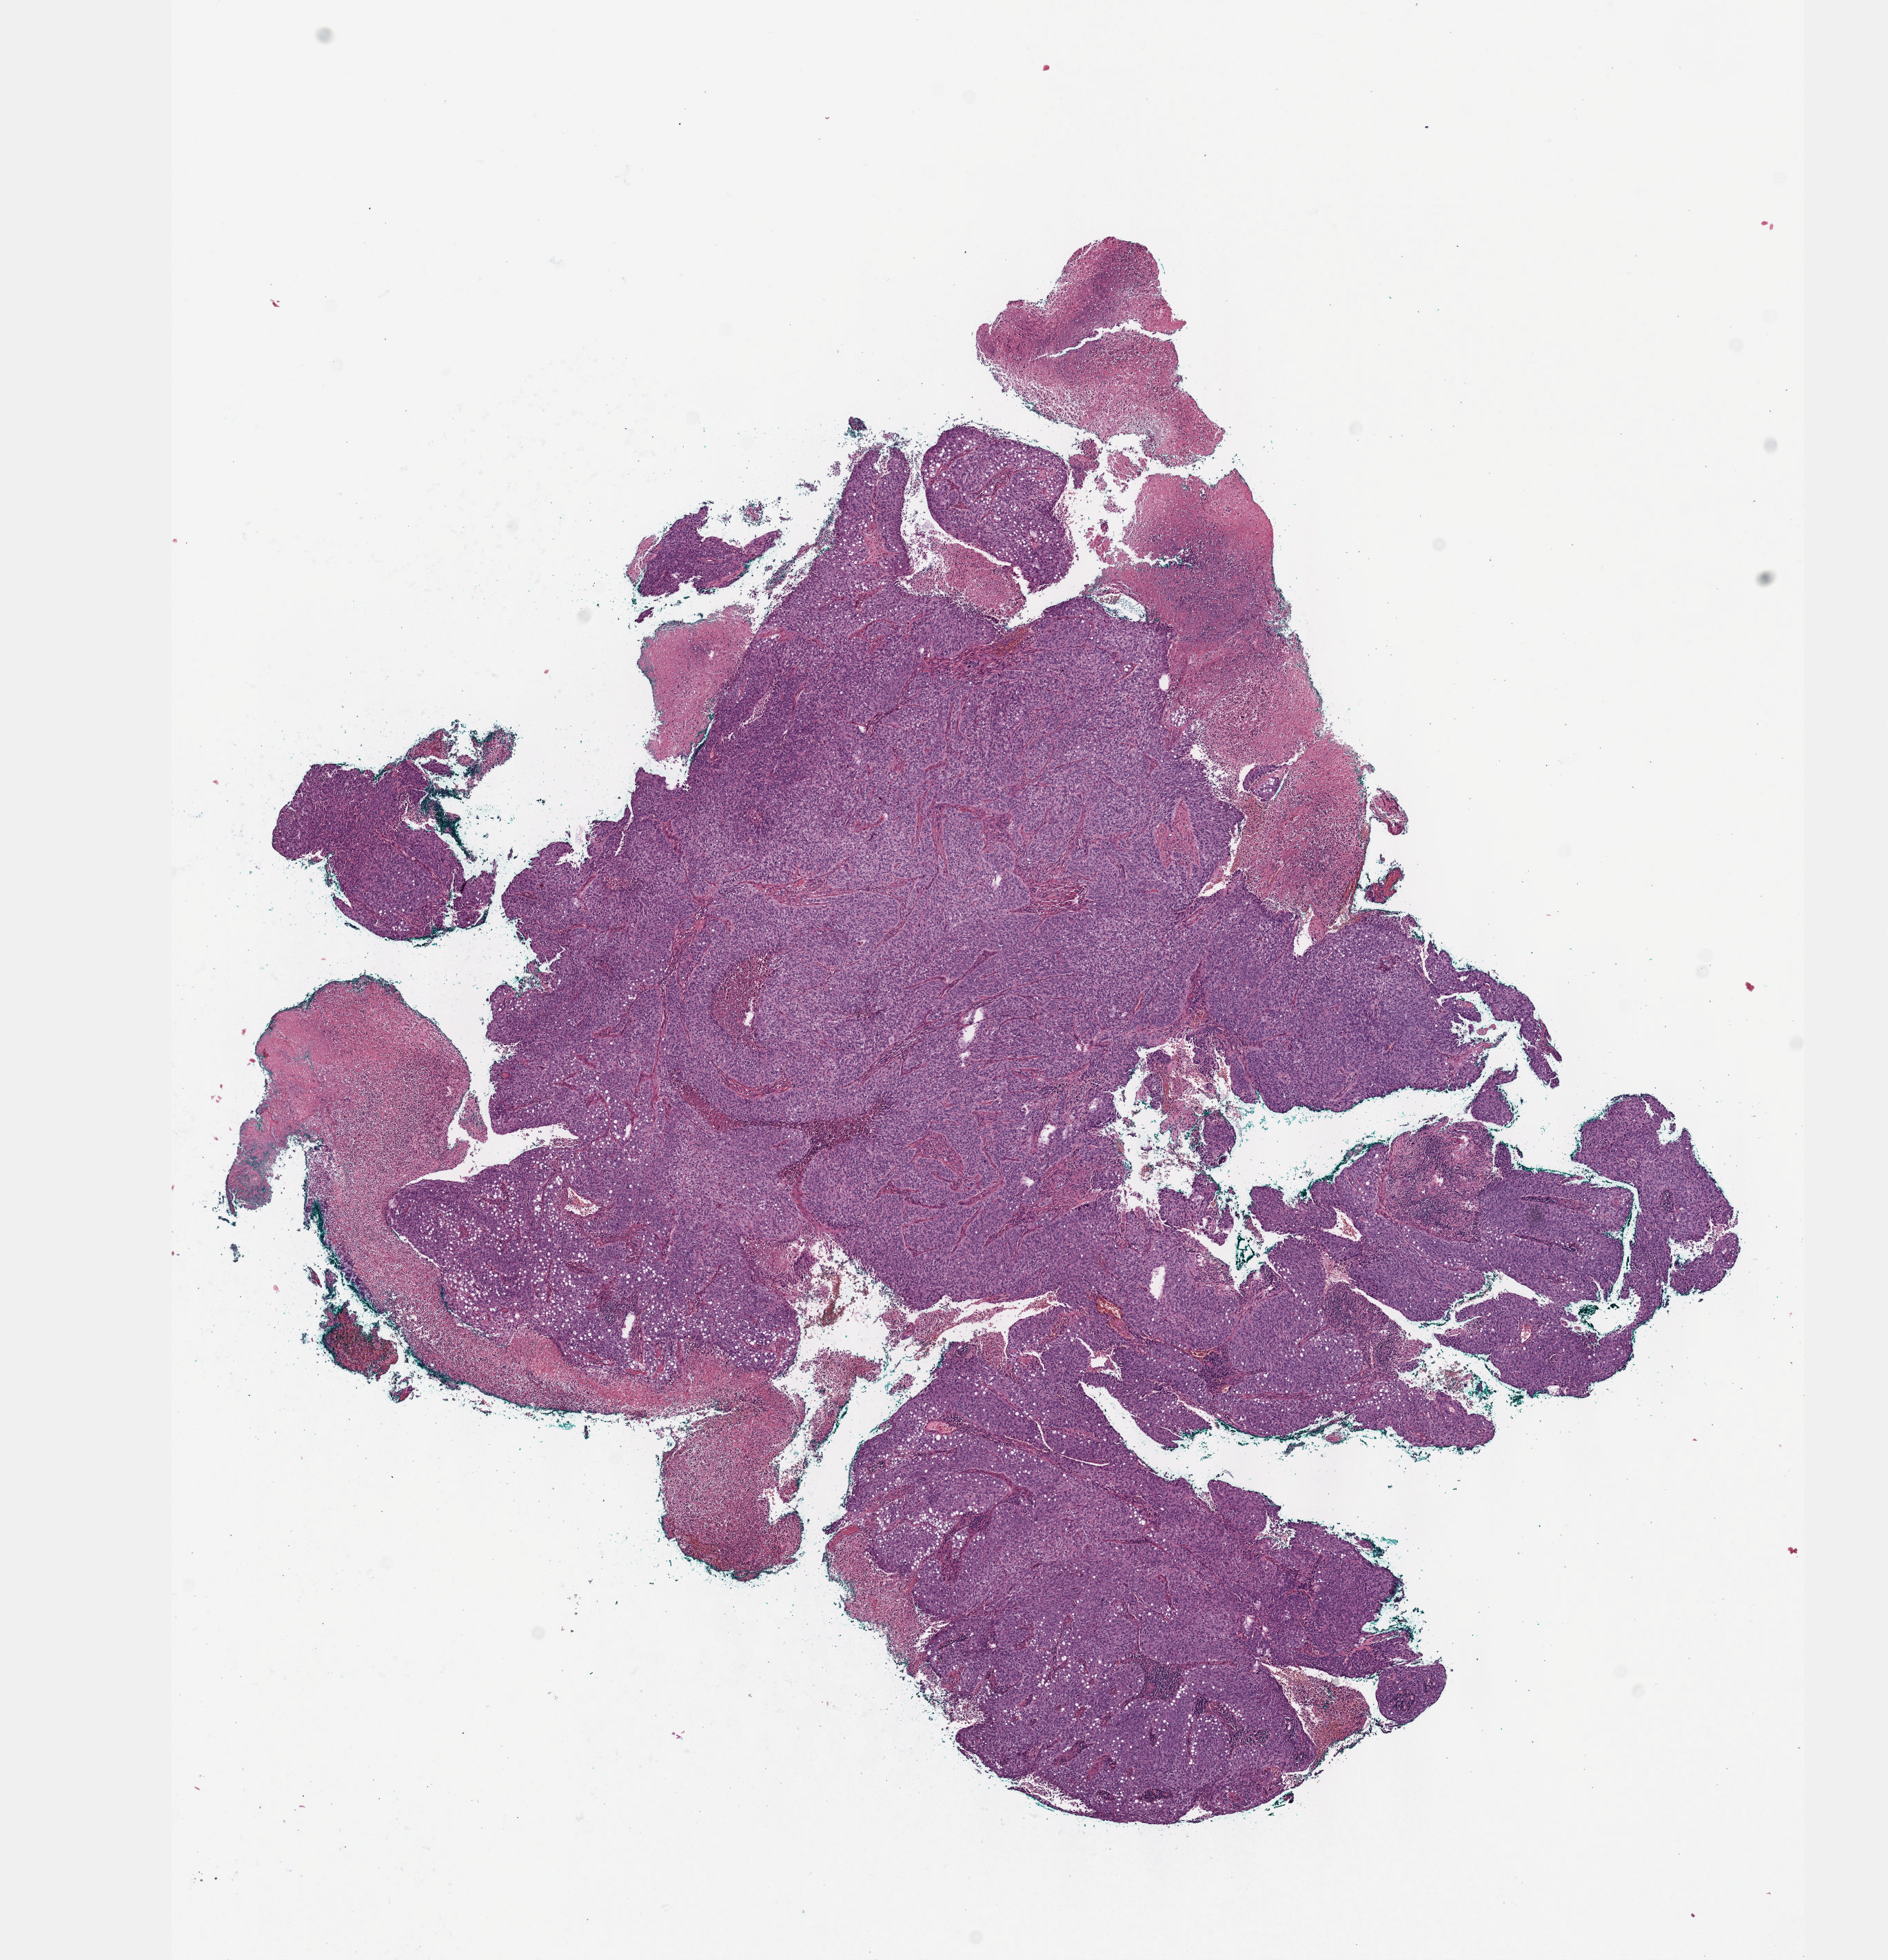
Digitized H&E tissue section (whole slide), shown as a low-resolution overview of the whole scanned area (about 11.1 x 11.5 mm, from a 40x scan); formalin-fixed paraffin-embedded (FFPE) diagnostic section; primary tumour sample from the cervix. Female, age 40 years at initial diagnosis. Histologic grade: G2 (moderately differentiated).
FIGO stage: IIB. Histologic diagnosis: Squamous cell carcinoma, NOS.